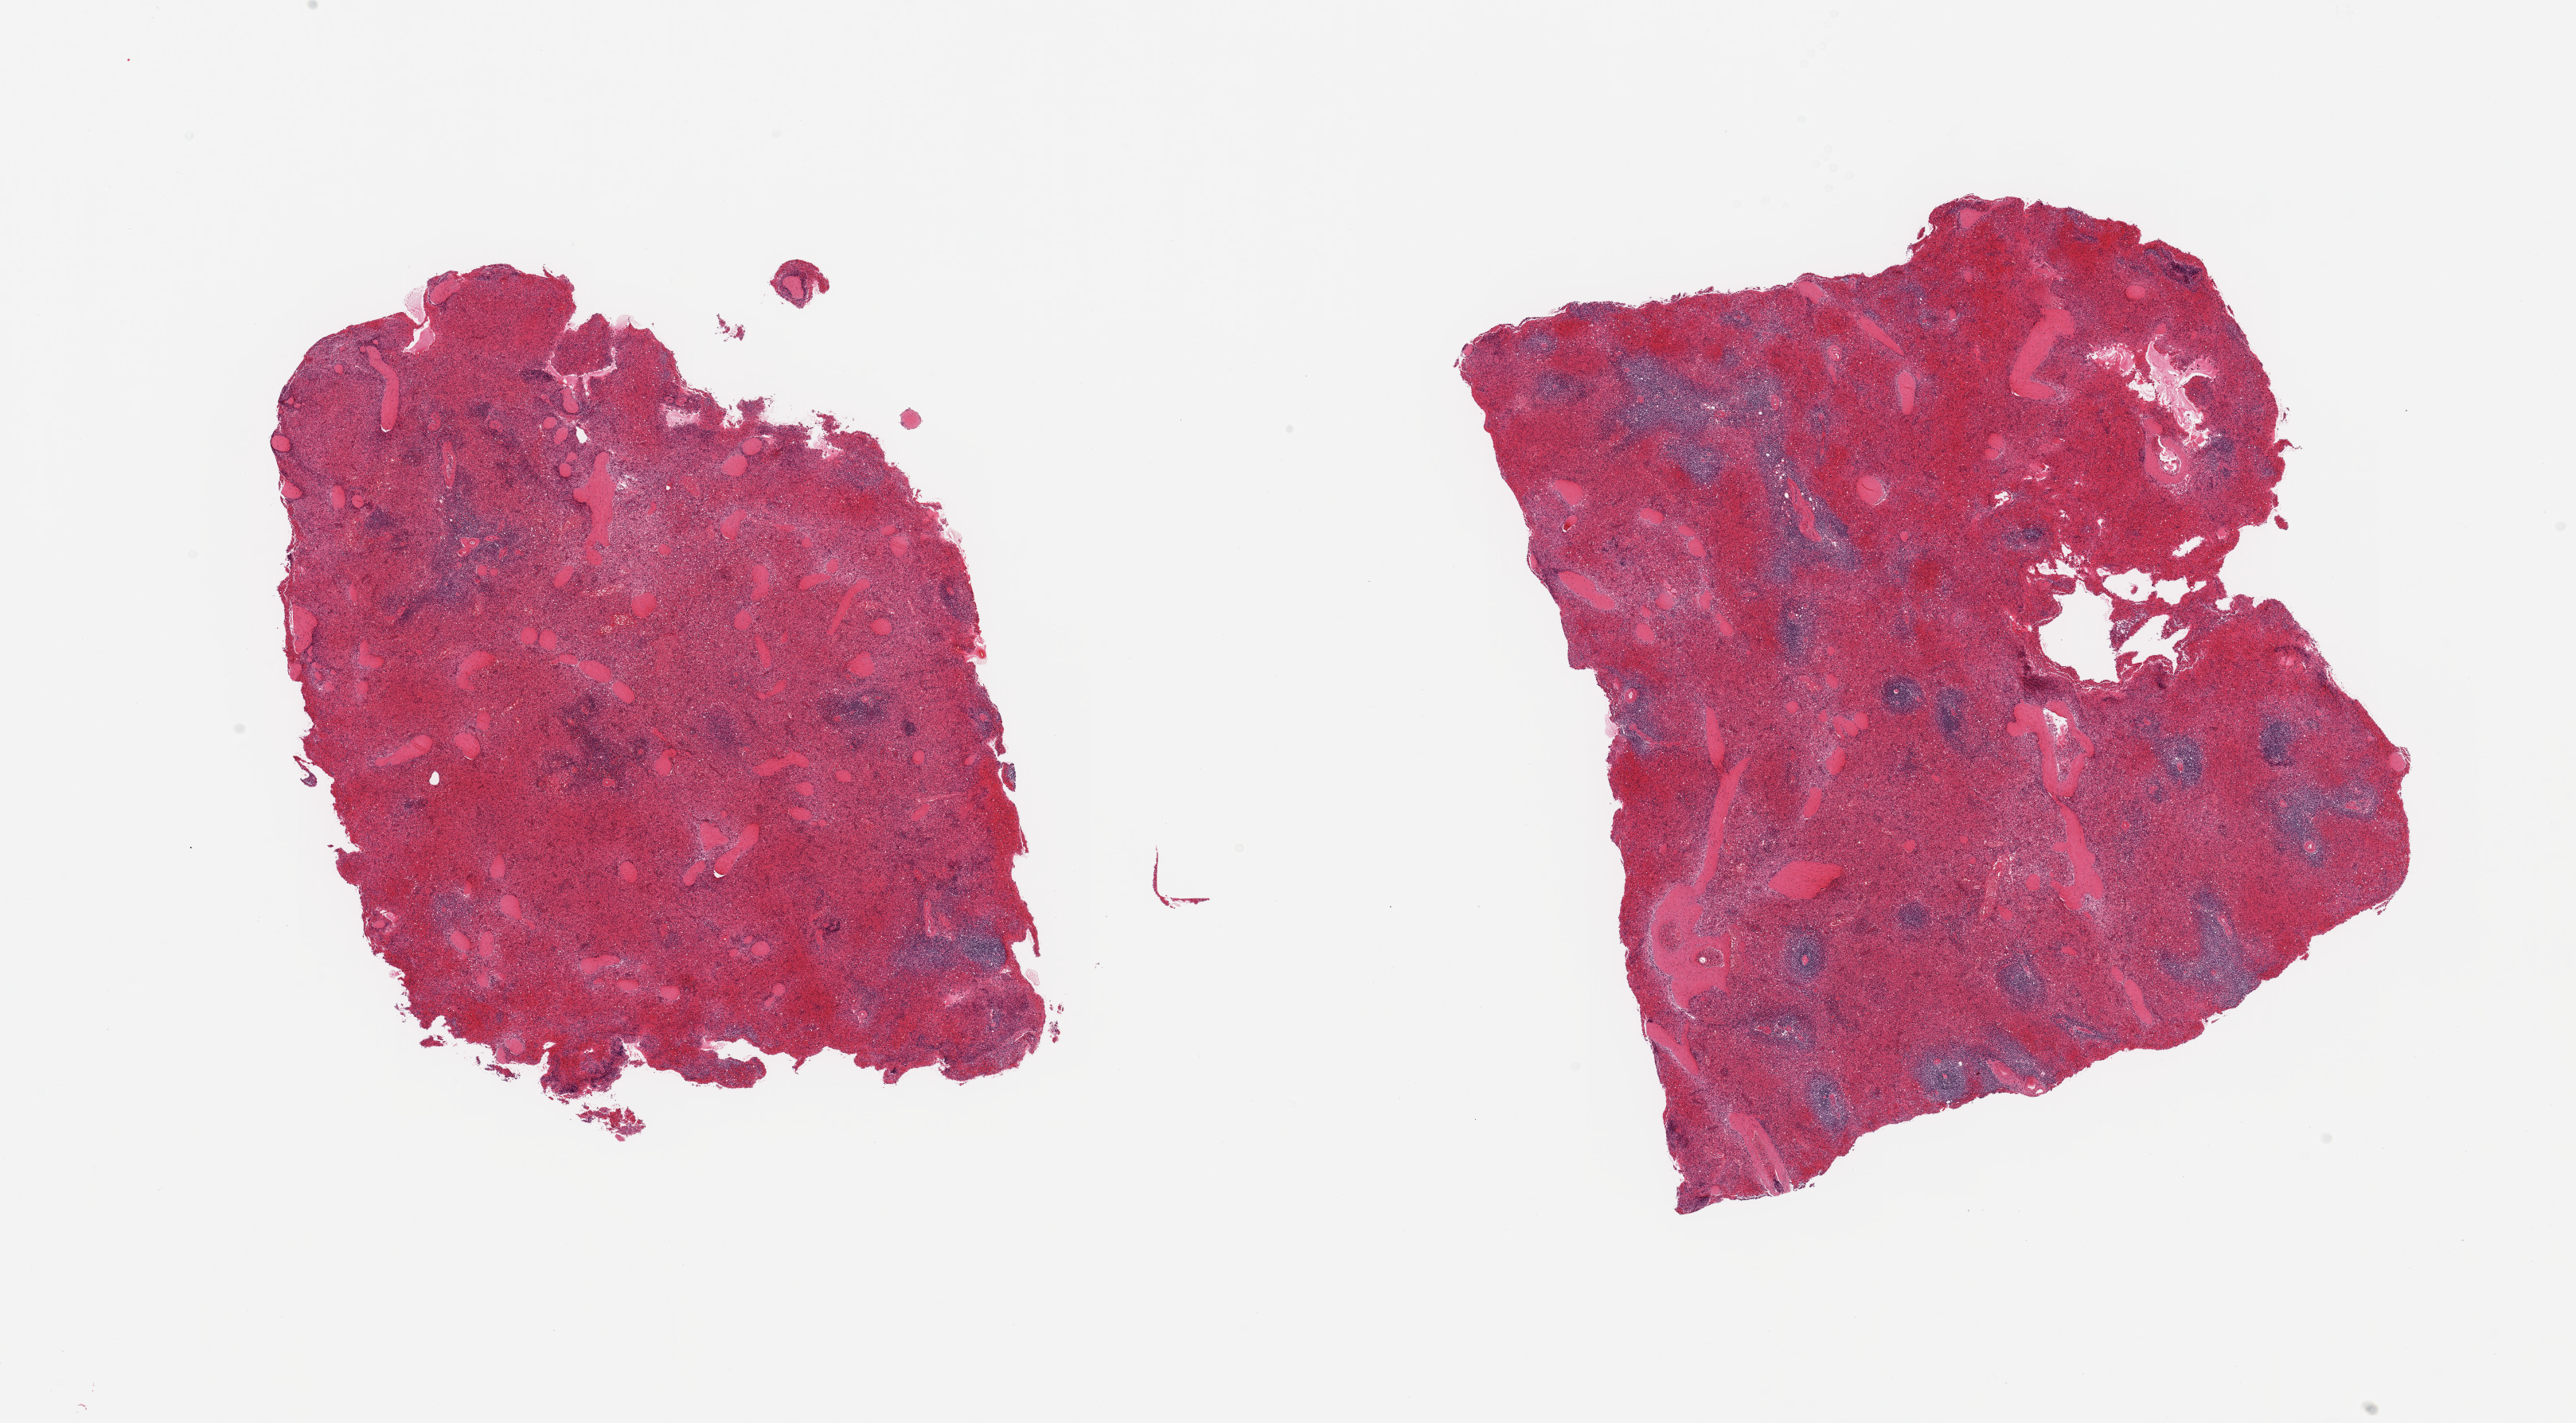
H&E whole-slide image, whole scanned area (about 25.6 x 14.1 mm) shown as a low-resolution overview. PAXgene-fixed paraffin-embedded (PFPE) section. Target tissue: spleen. Tissue donor sample. Donor: male.
Pathologist's review note for this sample: 2 pieces; marked congestion.